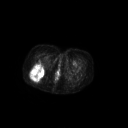
FDG PET of an extremity soft-tissue mass (from a PET/CT study), one axial slice. Position 51 of 267 along the scan axis. 3.27 mm slice thickness. 128 × 128 image matrix, field of view 700 × 700 mm. Female patient, age 70 years. Case-level facts recorded for this patient, not image findings: histological type: synovial sarcoma; grade: intermediate; site of the primary tumour: right buttock.
Structures marked on this image (expert contour drawn on MRI and transferred to this co-registered scan by the dataset authors):
- gross tumour volume including surrounding oedema: bounding box [x1, y1, x2, y2] px = [30, 63, 45, 81]
- gross tumour volume (mass): [30, 63, 45, 81]